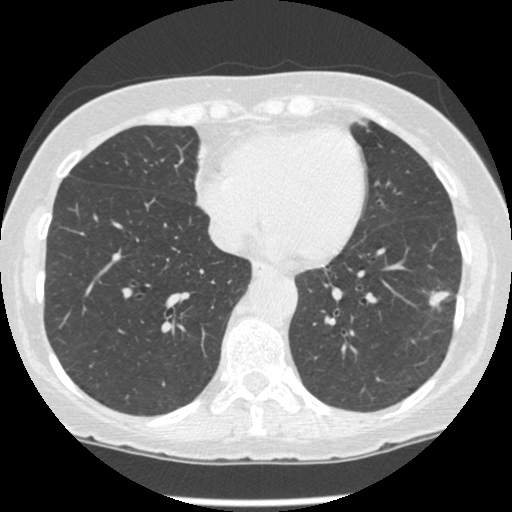
Low-dose screening chest CT, one axial slice; position 85 of 247 along the scan axis; 120 kVp; lung window (W 1500 / L -600 HU); 1.25 mm slice thickness; 512 × 512 image matrix, field of view 303 × 303 mm.
Annotated regions visible in this slice (outlined manually by an expert reader):
- lesion 1 (tumor, lower lobe of left lung): bounding box <430,290,450,308> (left, top, right, bottom; pixels)